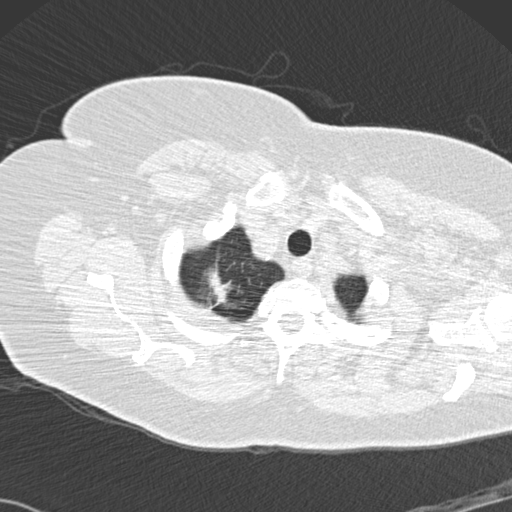
Low-dose screening chest CT, one axial slice; position 132 of 146 along the scan axis; reconstruction kernel B30f; lung window (W 1500 / L -600 HU); 2 mm slice thickness; 512 × 512 image matrix.
Outlined on this slice (outlined manually by an expert reader):
- lesion 1 (tumor, upper lobe of right lung): bounding box [x1, y1, x2, y2] px = [207, 267, 231, 304]